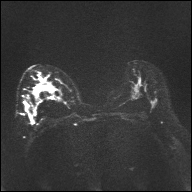
Breast MRI, one axial slice; position 18 of 32 along the scan axis; diffusion-weighted series; image 2 of 4 stored at this slice position (different b-values; order by instance number); 1.5 T; 4 mm slice thickness; 192 × 192 image matrix, field of view 360 × 360 mm. Female patient.
Outlined on this slice (manually delineated by an expert):
- tumour on diffusion-weighted imaging: bounding box (x1, y1, x2, y2) in pixels: (35, 83, 45, 89)